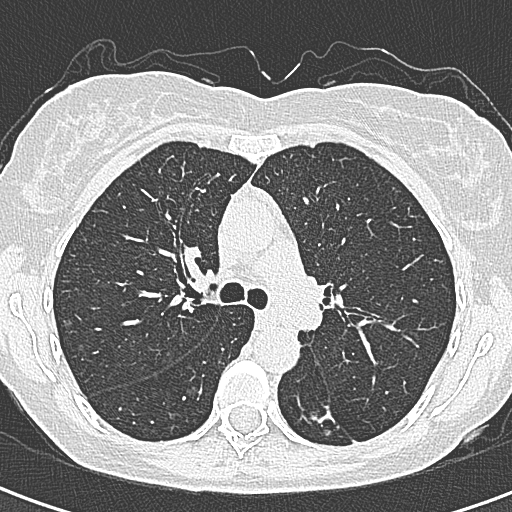
Chest CT (low-dose screening protocol), one axial image; baseline screening round; lung window (W 1500 / L -600 HU); 120 kVp. Female participant, aged 58 years at enrolment. Former smoker at enrolment.
Expert-annotated lung lesion, bounding box [x1, y1, x2, y2] px = [289, 391, 360, 455]. The screening reader recorded 2 non-calcified nodules or masses ≥4 mm on this exam (left lower lobe, right lower lobe); which of them this box marks is not recorded. Official screen result: positive, change unspecified: nodule(s) >= 4 mm or enlarging nodule(s), mass(es), or other non-specific abnormalities suspicious for lung cancer. Lung cancer was diagnosed 22 days after this screen: adenocarcinoma, NOS, left lower lobe, moderately differentiated (G2), stage IA (AJCC 6th edition), 25 mm at pathology.